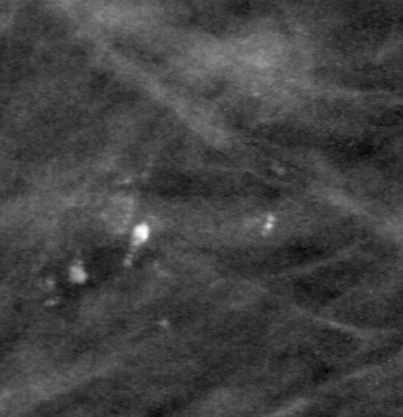
Region of interest cut from a scanned film mammogram (one marked finding), left breast, MLO view, BI-RADS breast density category 2 (scale 1–4).
- Finding: calcifications, morphology pleomorphic, distribution clustered; BI-RADS assessment category 4; pathology (as recorded): benign.